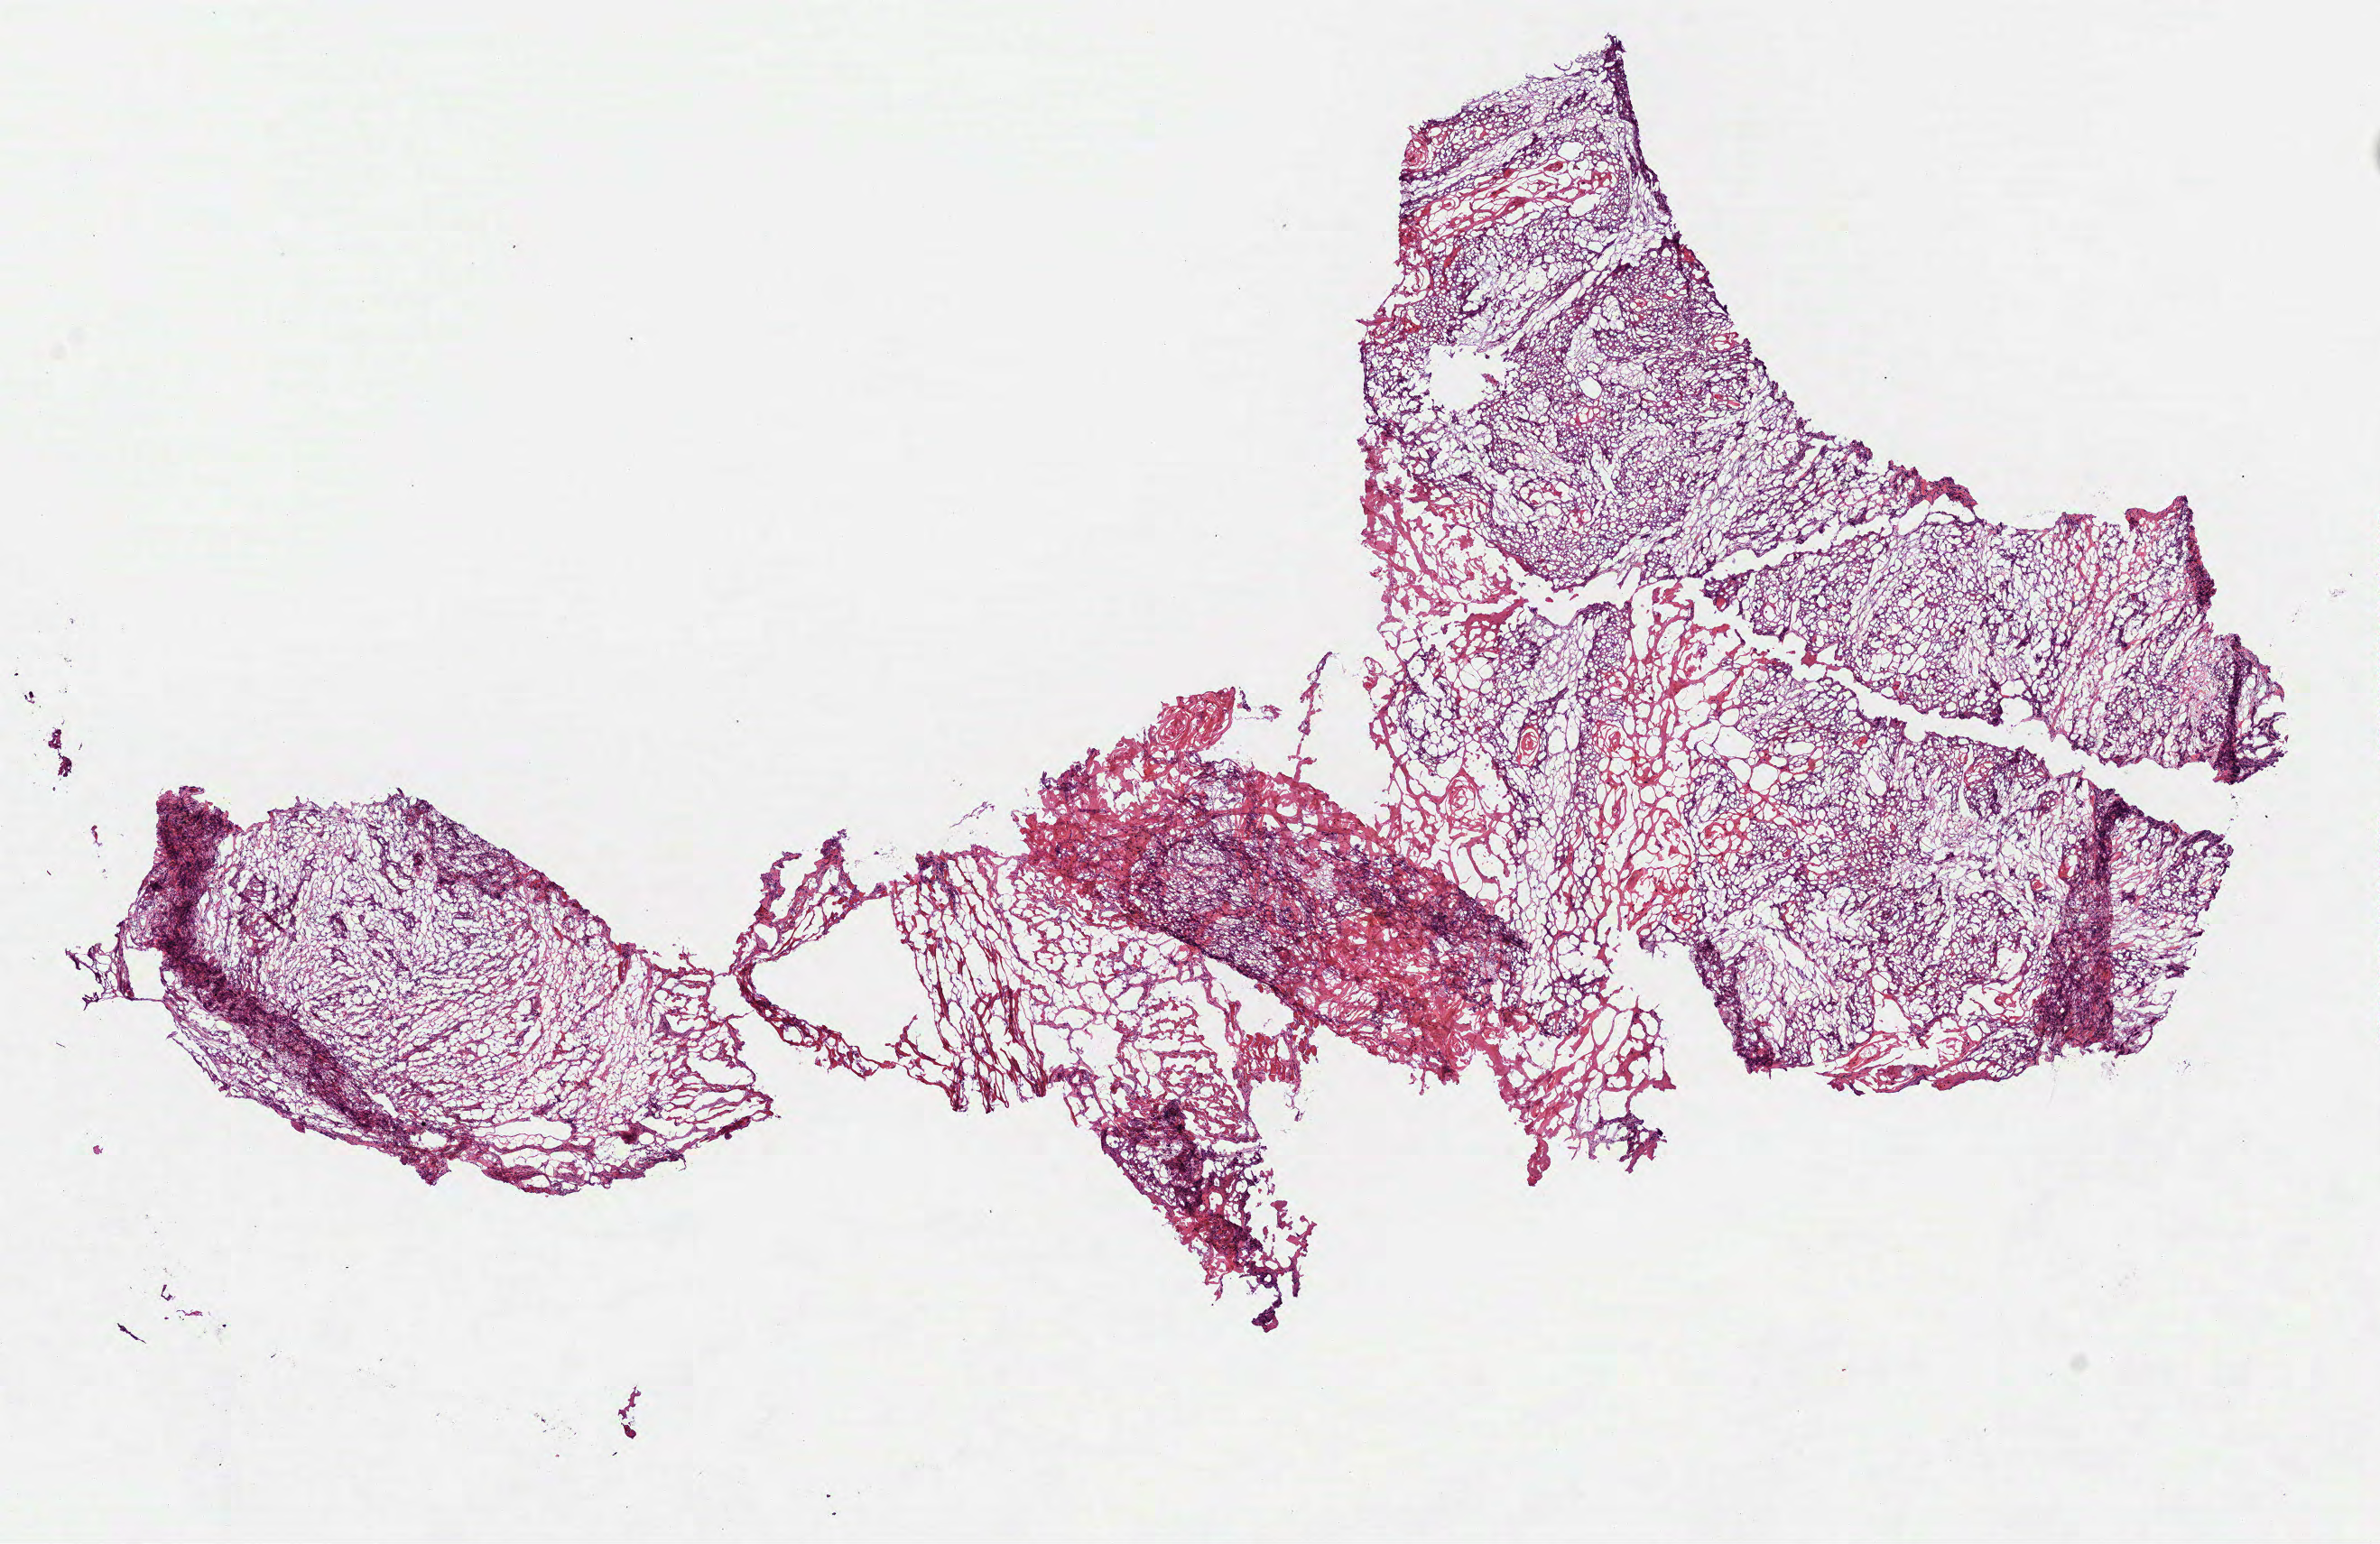
H&E whole-slide image — a low-resolution overview of the entire scanned area, about 10.6 x 6.9 mm (acquisition: 40x scan). Frozen section. Head and neck, primary tumour sample. Male, age 67 years at initial diagnosis. Histologic grade: G2 (moderately differentiated). Composition of this section per pathologist review: tumour cells 90%, tumour nuclei 80%, normal cells 0%, stromal cells 0%, necrosis 10%. Infiltration values recorded for this section: lymphocyte infiltration 2%, monocyte infiltration 0%, neutrophil infiltration 0%.
- AJCC pathologic stage: III (7th edition)
- diagnosis: Squamous cell carcinoma, NOS (tongue, NOS)
- TNM: T3 N1